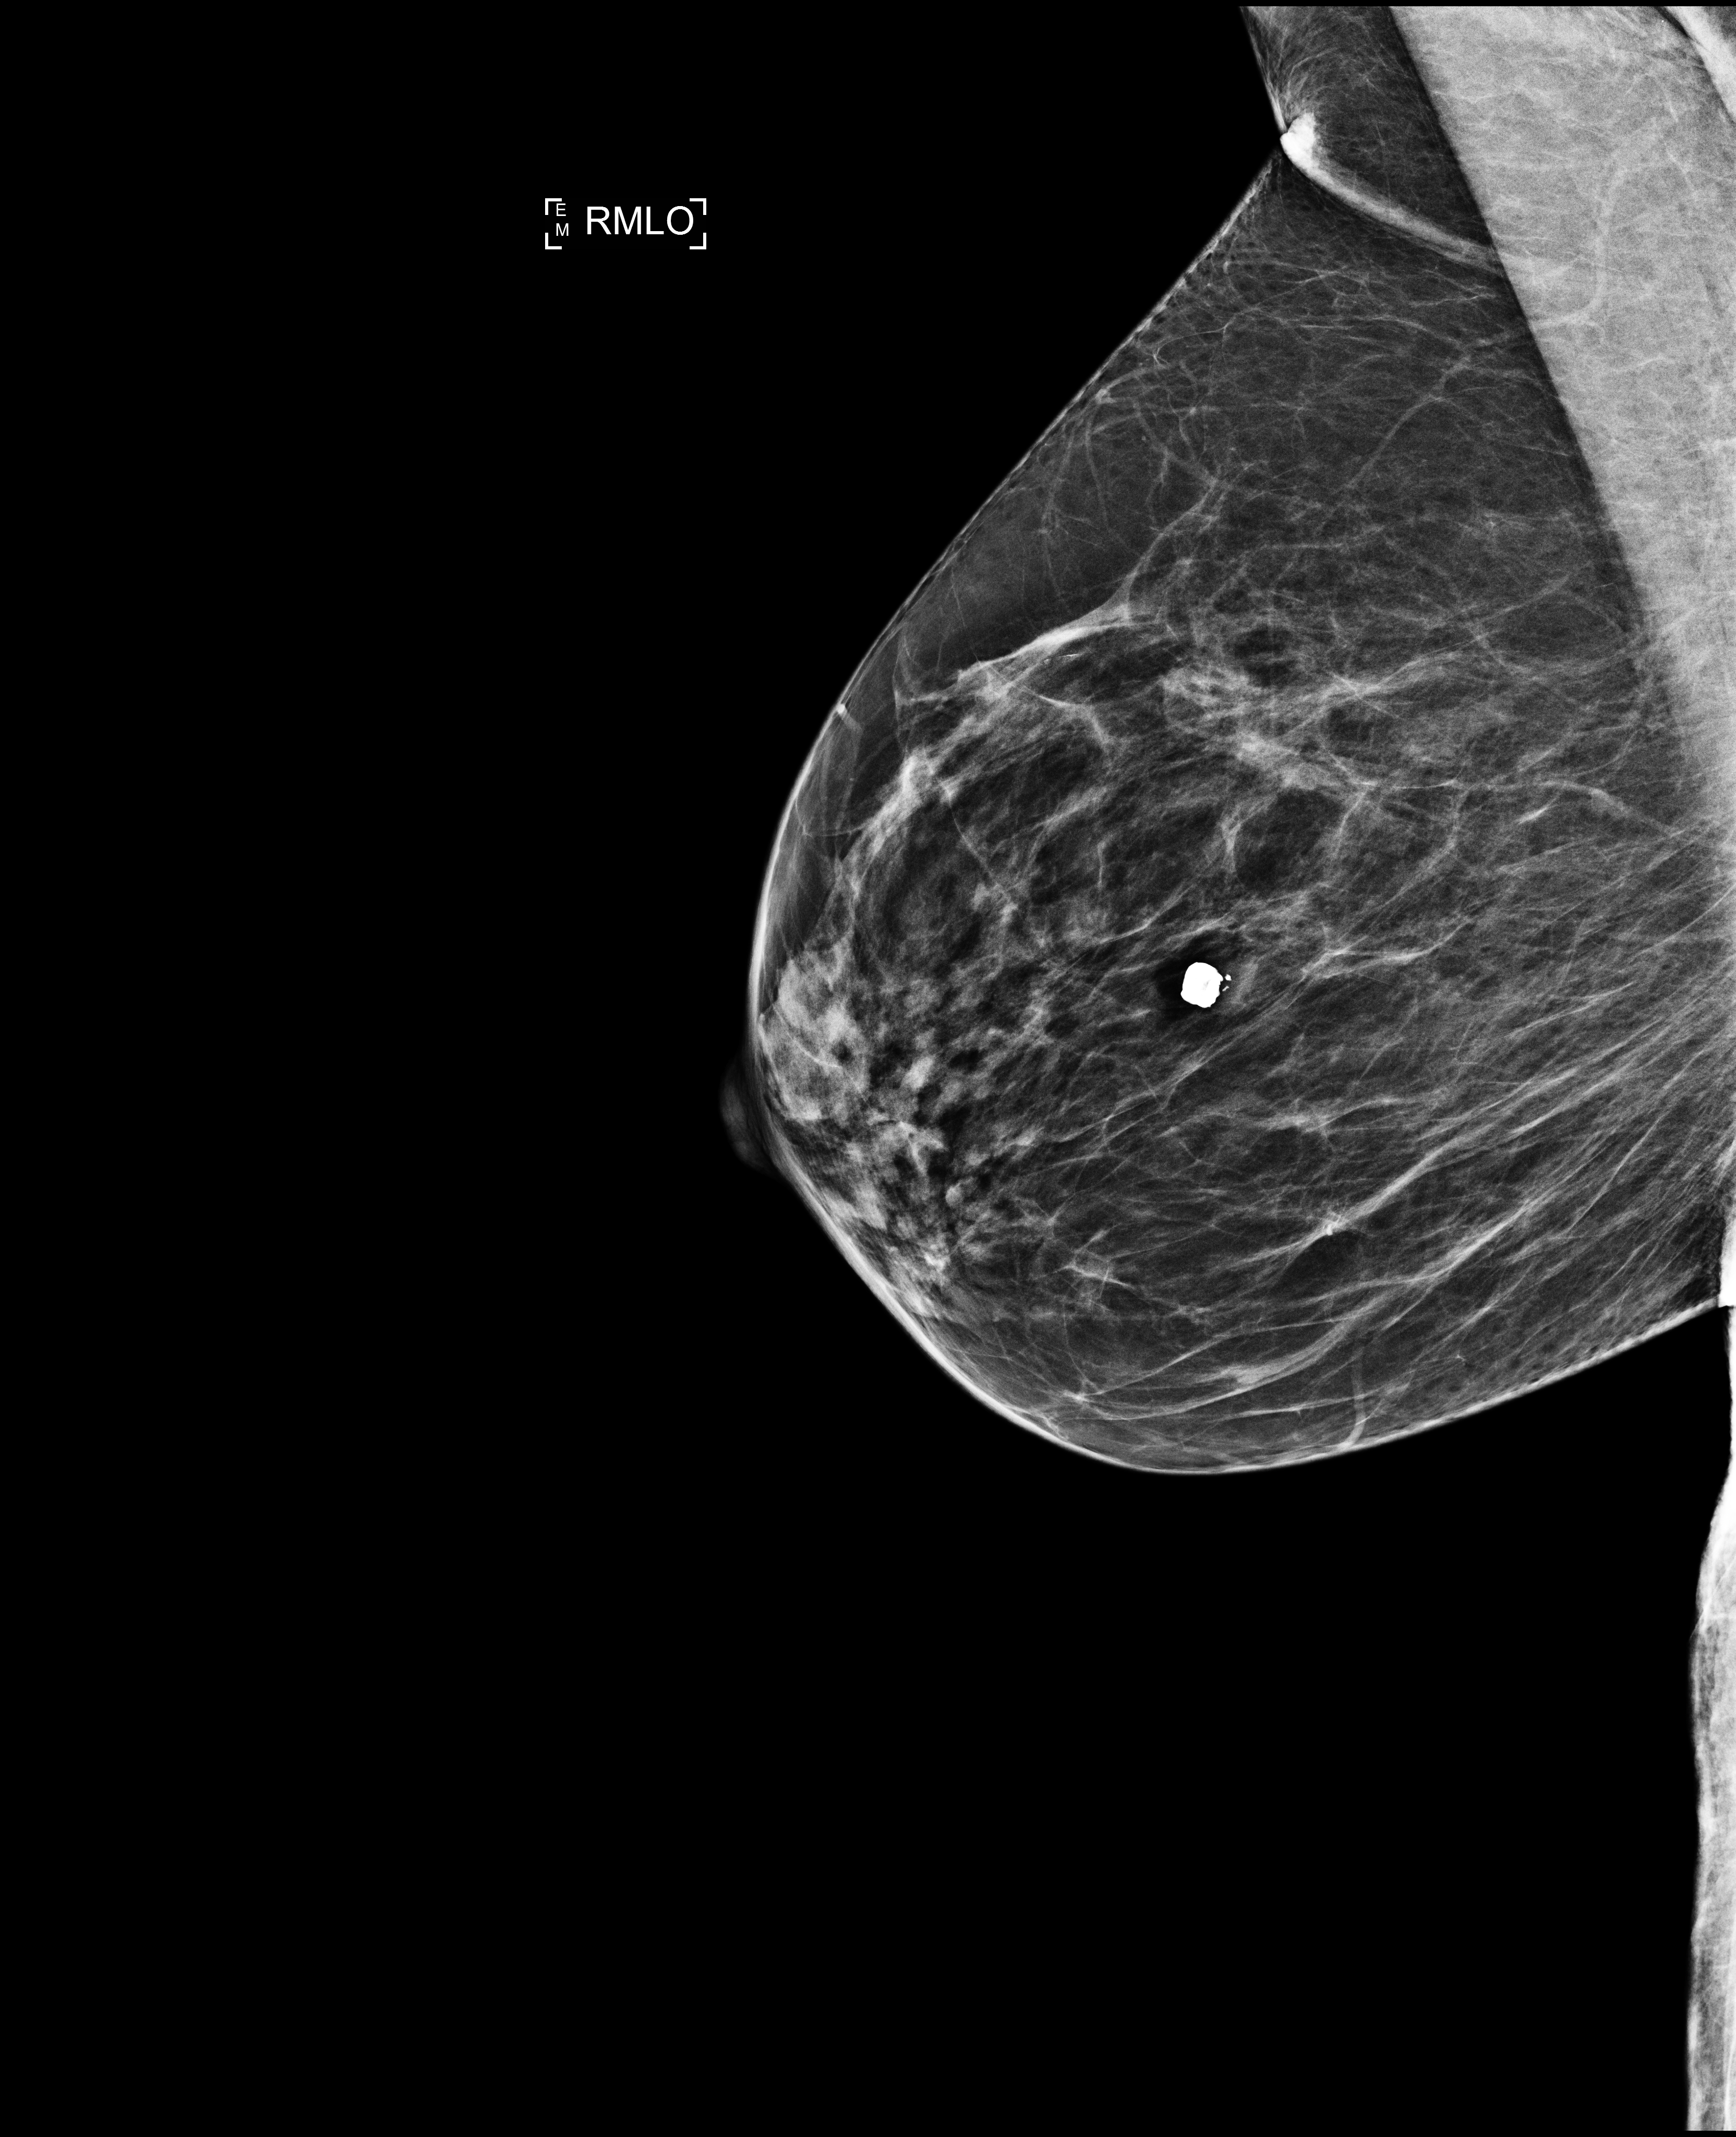
Annual screening mammography examination, compressed breast thickness 49 mm. Female patient, age 65 years.
Image type: full-field digital mammogram. Breast: right. Projection: MLO view.